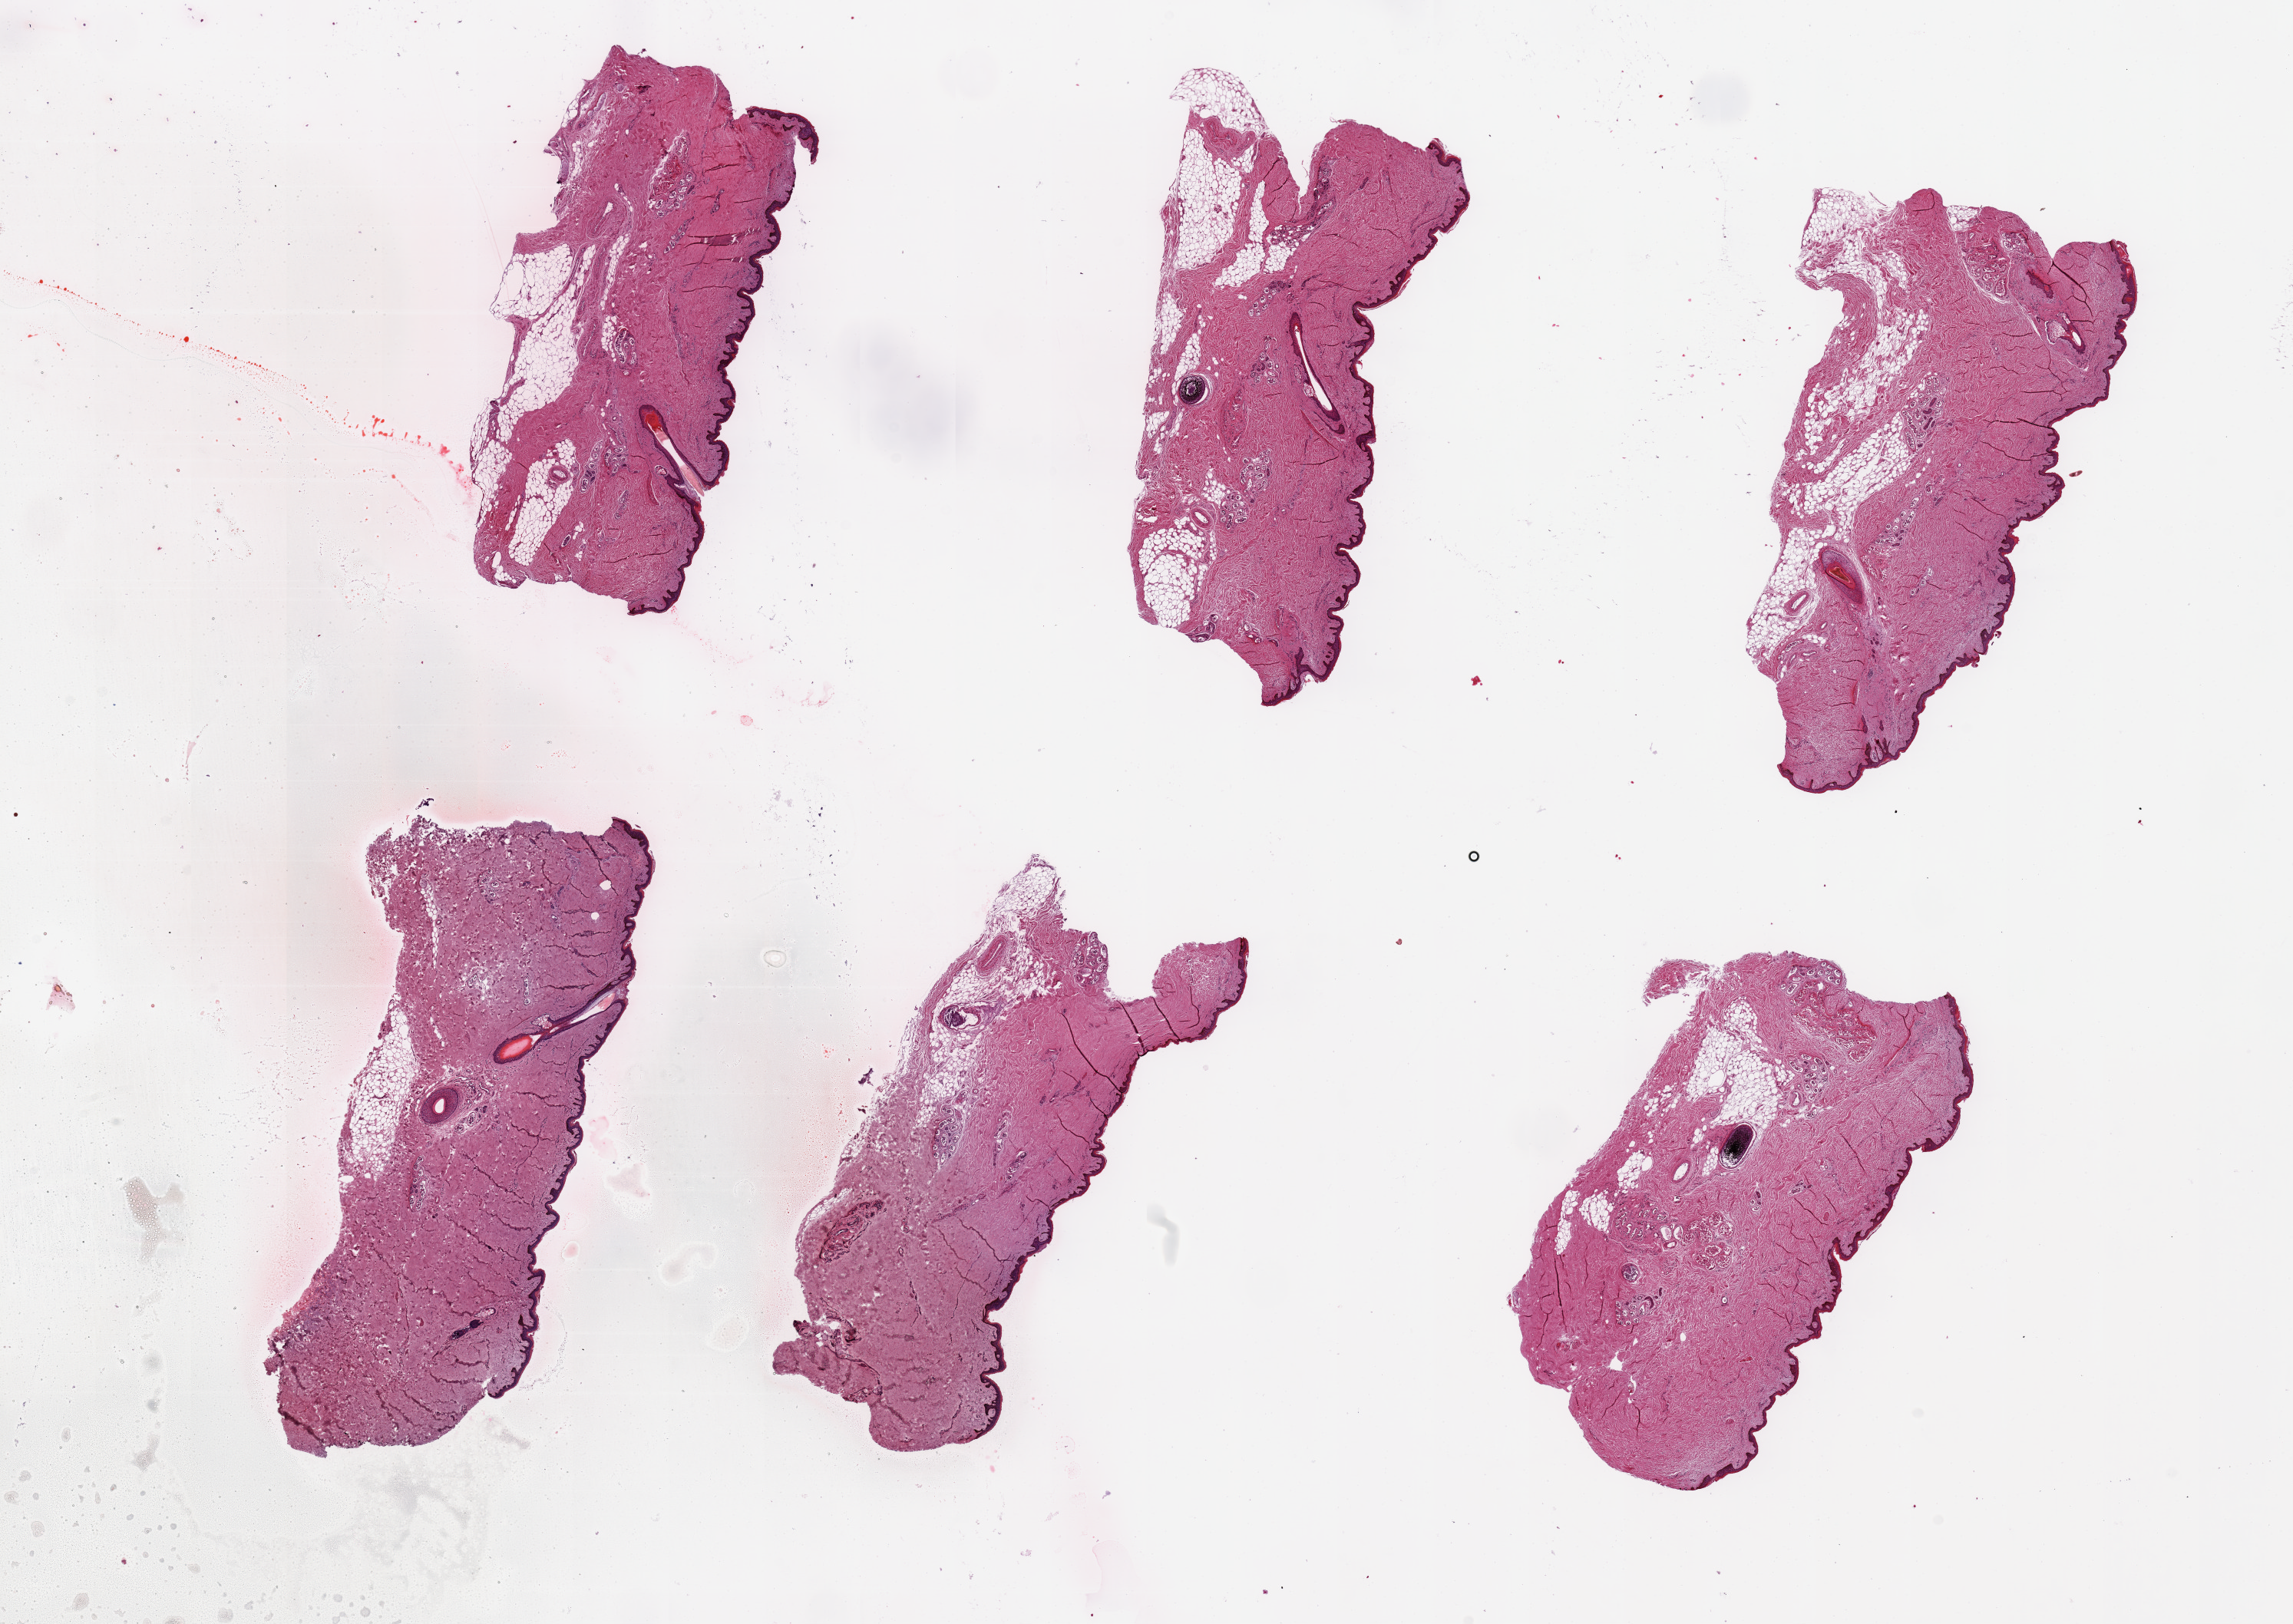
Digitized H&E-stained section — low-resolution overview of the scanned area, about 23.6 x 16.7 mm; PAXgene-fixed paraffin-embedded (PFPE) section; target tissue: skin of suprapubic region; donor tissue sample. Donor: male.
• review note (as recorded): 6 pieces, up to 7x3mm; Up to 1 mm subcutaneous adipose